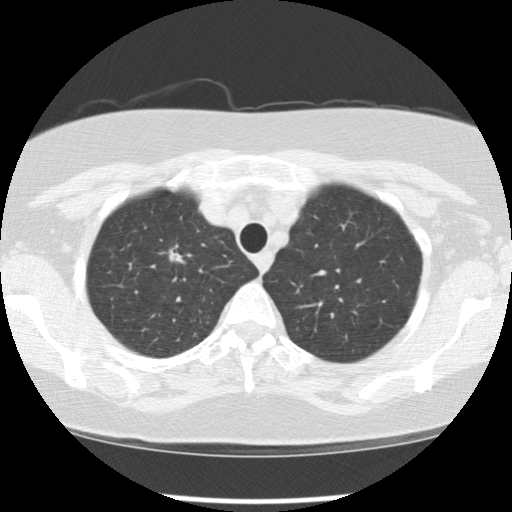
Low-dose screening chest CT, one axial slice; slice 94 of 113 in the series (ordered by position); reconstruction kernel STANDARD; 120 kVp; lung window (W 1500 / L -600 HU); 2.5 mm slice thickness; 512 × 512 image matrix.
Annotated regions visible in this slice (expert manual segmentation):
- lesion 1 (tumor, upper lobe of right lung): bounding box <168,247,183,263> (left, top, right, bottom; pixels)